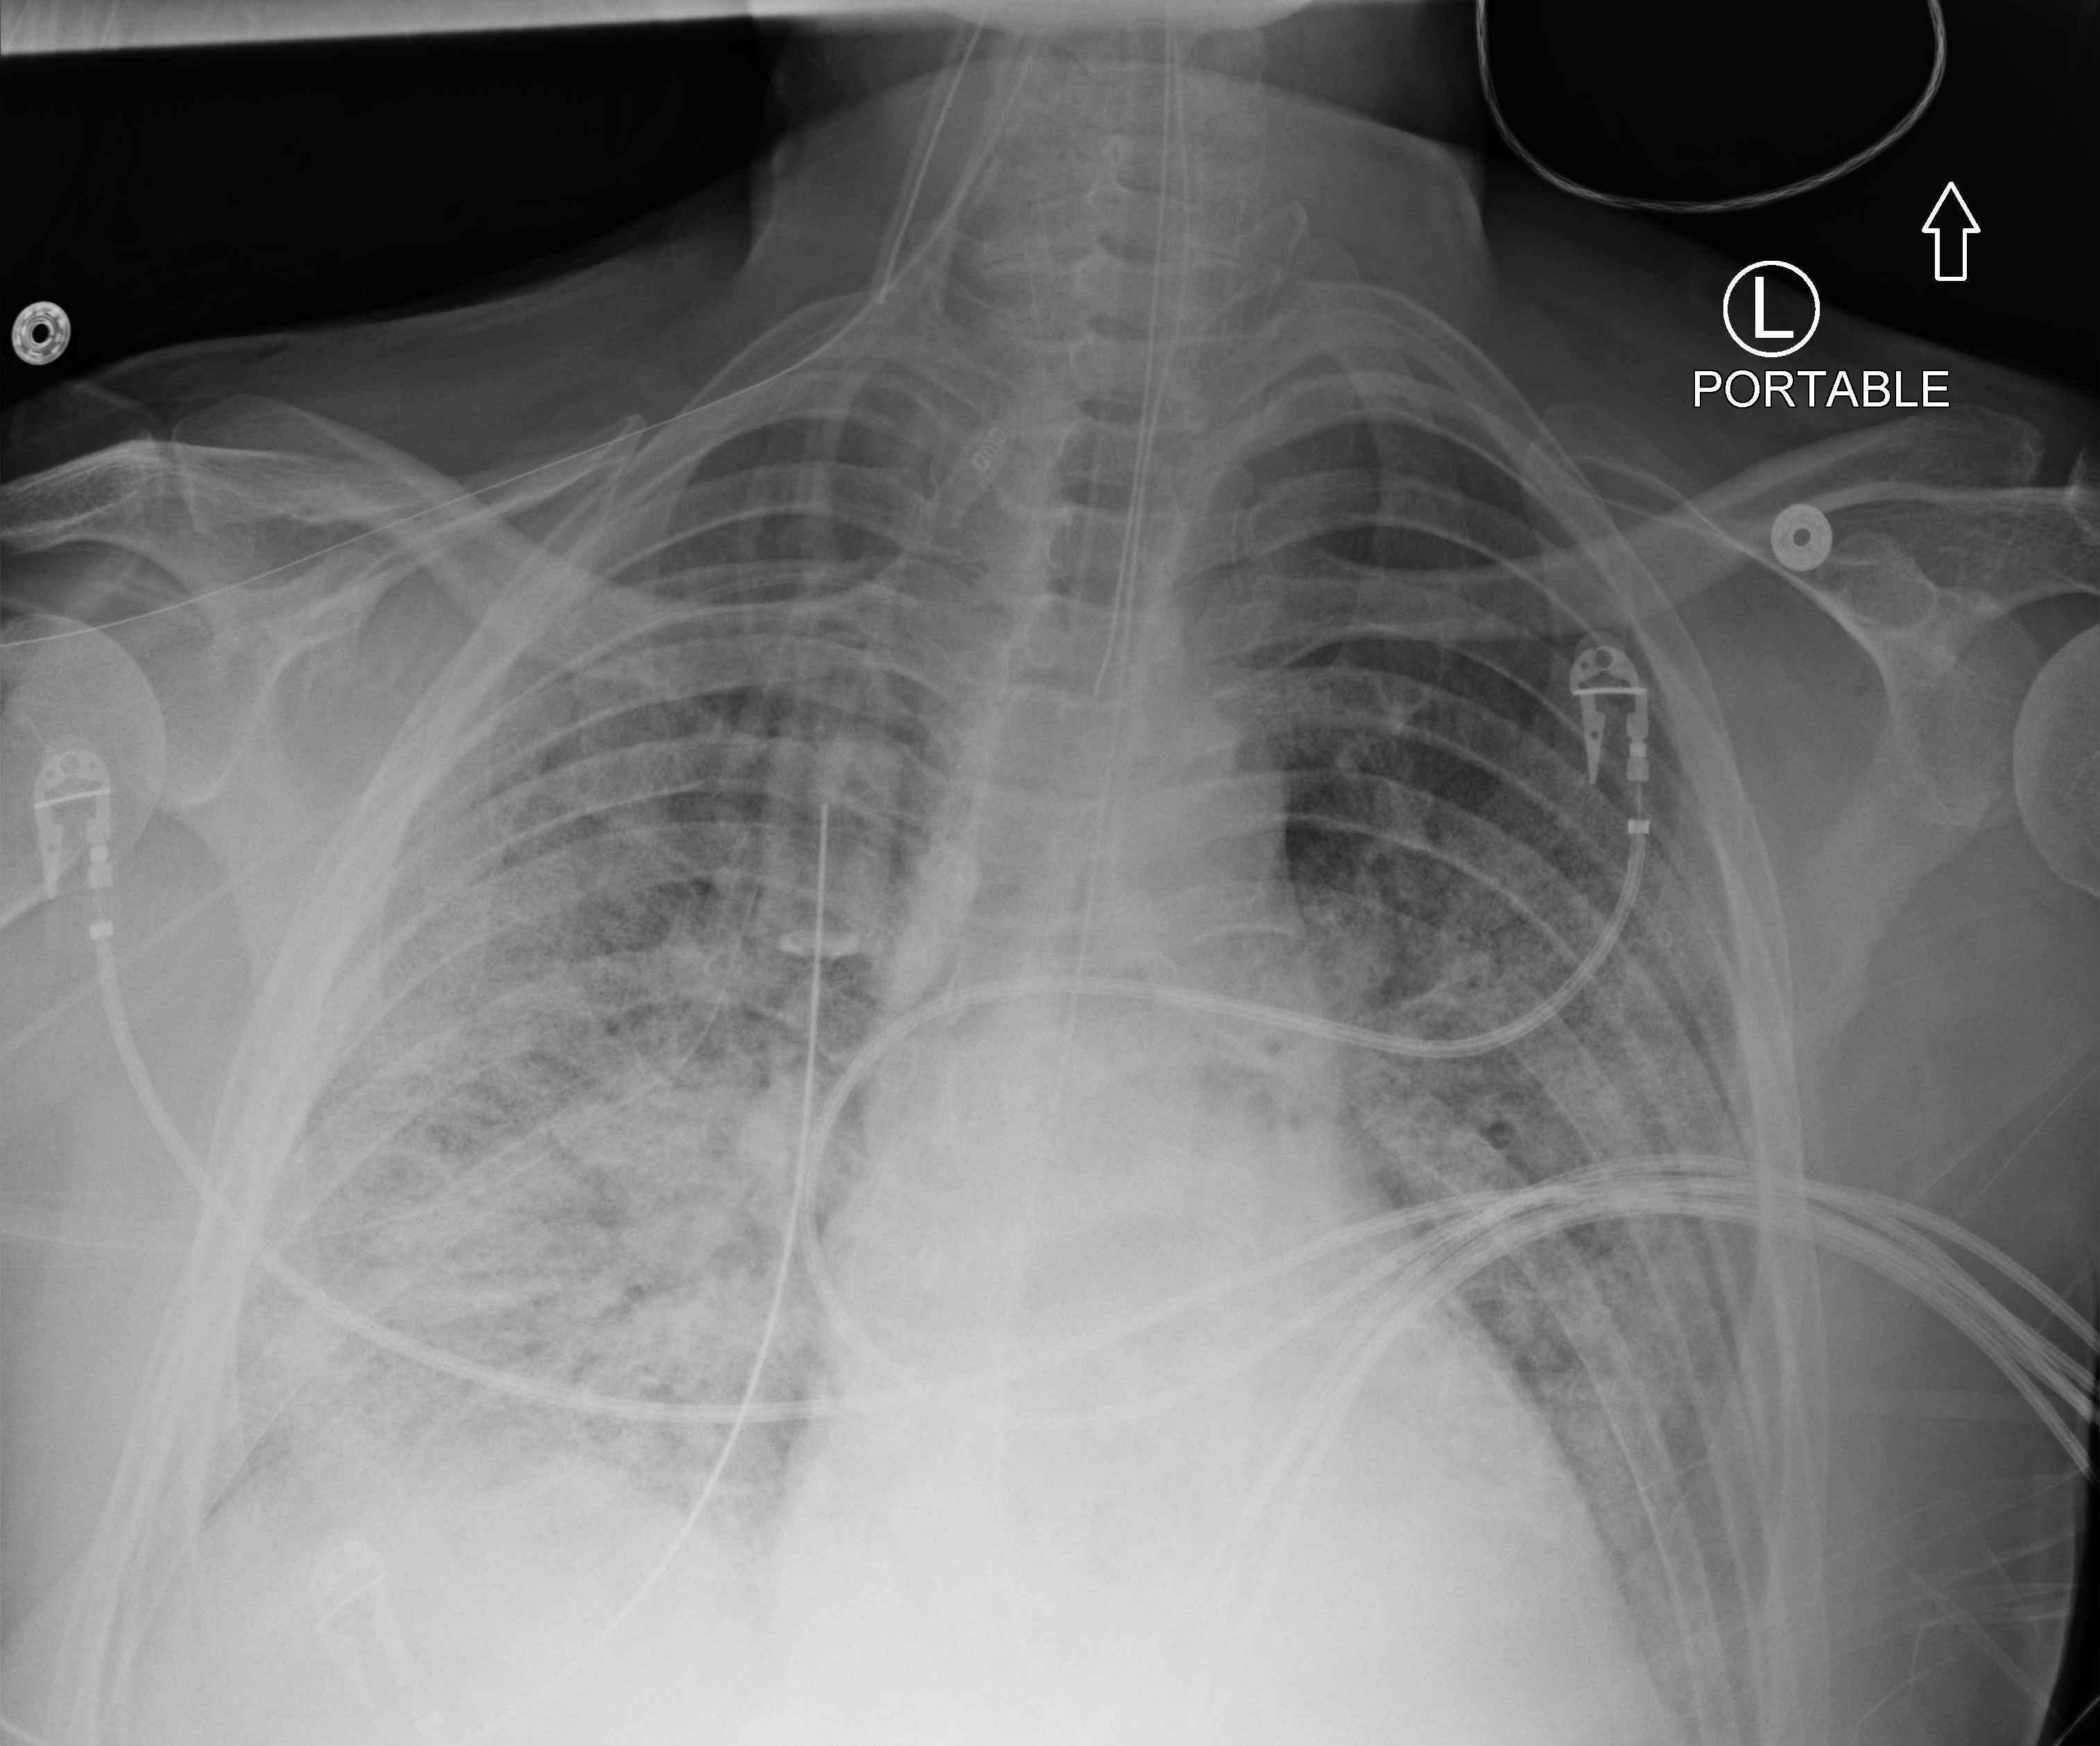
Bedside chest radiograph (computed radiography), anteroposterior (AP) projection. Male patient hospitalised with COVID-19, age 18–59 years.
Admission-level facts for this patient (not findings on this image; timing relative to this image not recorded): admitted to intensive care during this hospital stay: yes.